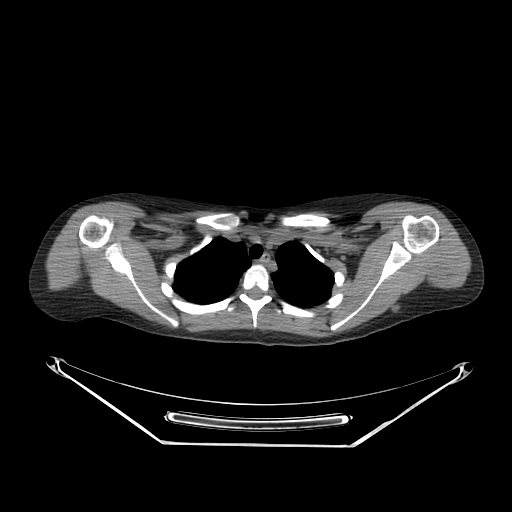
CT of an extremity soft-tissue mass (from a PET/CT study), one axial slice; slice 211 of 267 in the series (ordered by position); reconstruction kernel SOFT; soft-tissue window (W 400 / L 40 HU); 512 × 512 image matrix, field of view 500 × 500 mm. Female patient. From the clinical record (not read from this slice): histological type: malignant fibrous histiocytoma; grade: low; site of the primary tumour: left arm.
Structures marked on this image (expert contour drawn on MRI and transferred to this co-registered scan by the dataset authors):
- gross tumour volume (mass): box from (x=429, y=256) to (x=453, y=282) px